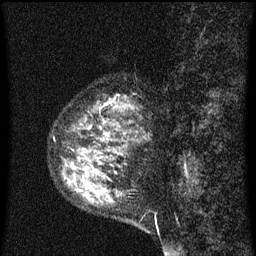
Breast MRI (dynamic contrast-enhanced), one sagittal slice. Position 22 of 60 along the scan axis. Dynamic contrast-enhanced series, image 2 of 3 at this slice position (ordered by acquisition). 1.5 T. TE 4.2 ms, TR 8 ms. 2 mm slice thickness. 256 × 256 image matrix, field of view 180 × 180 mm. Female patient, age 55 years.
Annotated regions visible in this slice (semi-automatically segmented with operator editing):
- analysis volume of interest (the breast-tissue region the enhancement analysis was run in; not a lesion): bounding box <56,102,149,151> (left, top, right, bottom; pixels)
- tumour enhancement mask (voxels above the 70 % enhancement threshold inside the analysis volume of interest): <90,104,119,141>